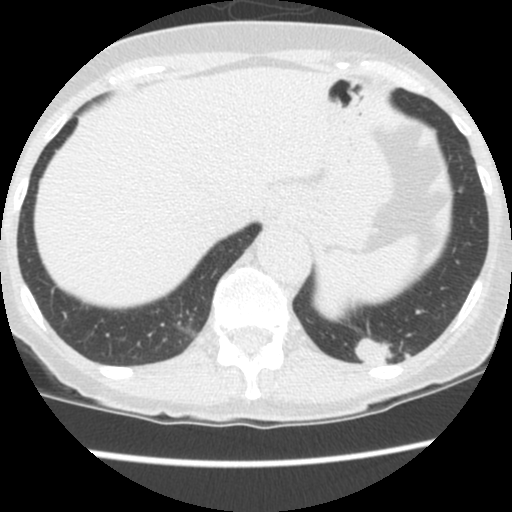
Low-dose screening chest CT, one axial slice; position 25 of 130 along the scan axis; 120 kVp; lung window (W 1500 / L -600 HU); 512 × 512 image matrix, field of view 290 × 290 mm.
Outlined on this slice (expert manual segmentation):
- lesion 1 (tumor, lower lobe of left lung): box from (x=356, y=337) to (x=395, y=367) px